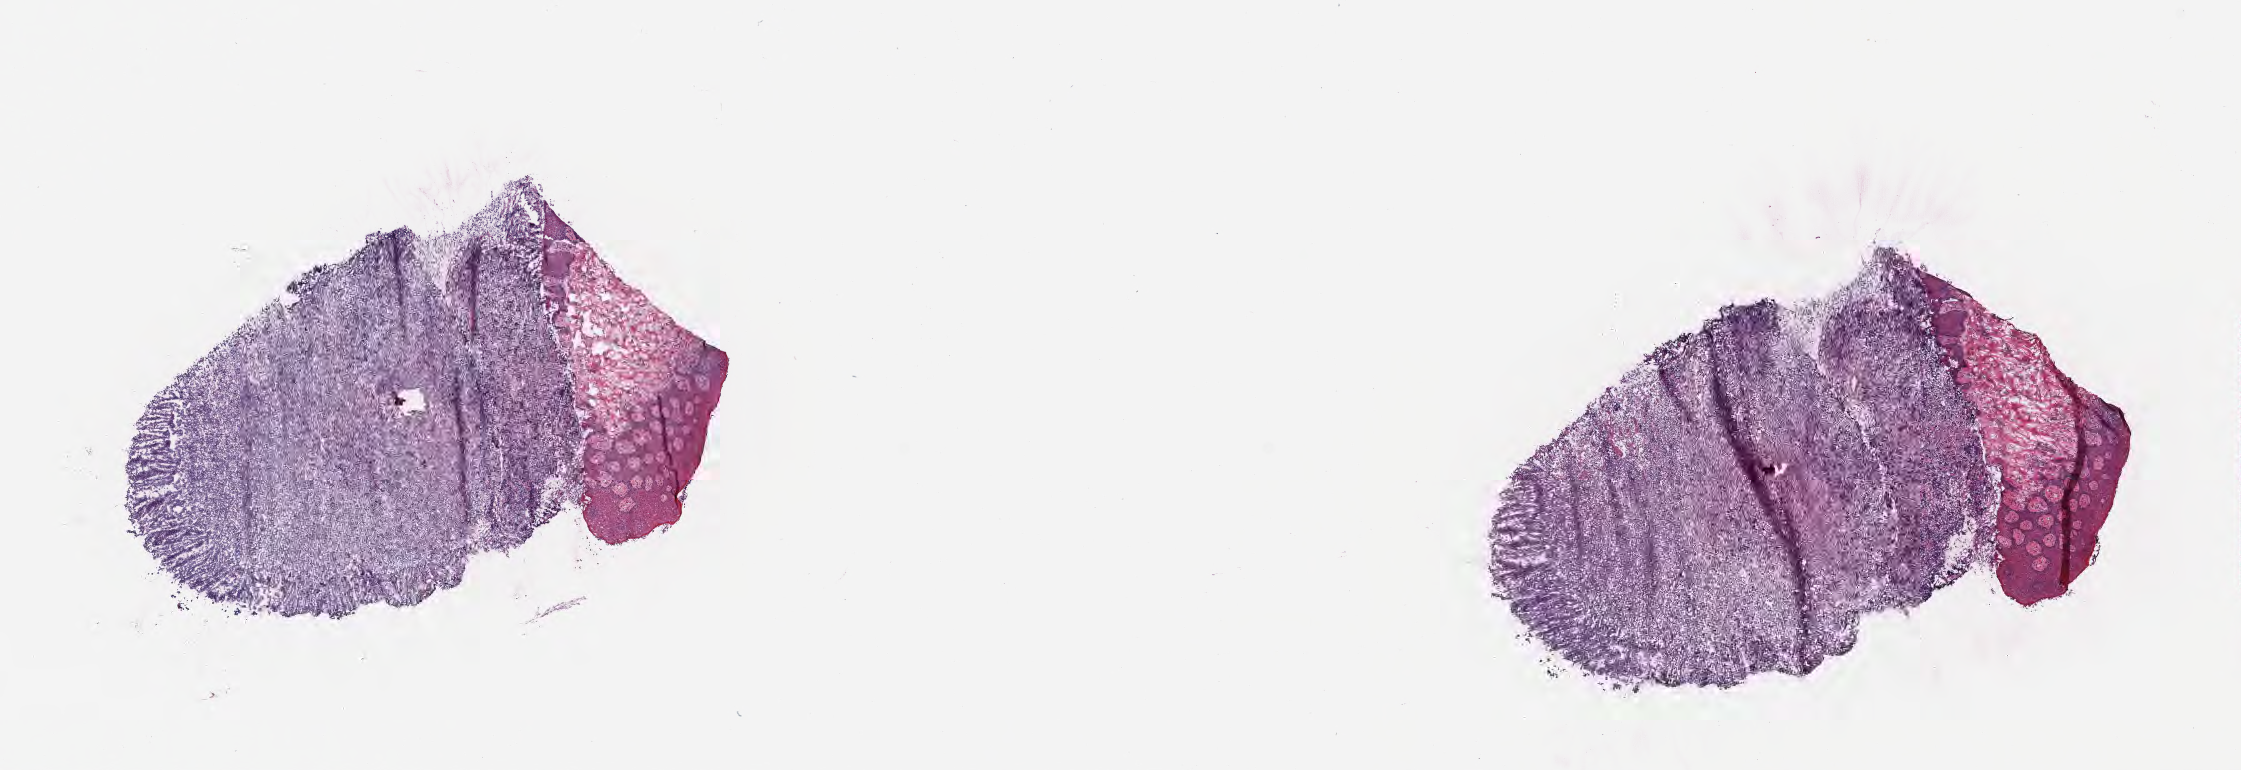
Haematoxylin and eosin whole-slide image, shown as a low-resolution overview of the whole scanned area (about 18.1 x 6.2 mm), frozen section (tissue freezing medium), specimen: primary tumor, site: gum of mandible. Male patient, aged 10. Slide review estimates, as recorded: tumor cells 70%, tumor nuclei 80%, stromal cells 10%, necrosis 10%, normal cells 10%. Infiltration values recorded for this section: lymphocyte infiltration 40%, monocyte infiltration 15%, neutrophil infiltration 5%.
• diagnosis: Burkitt lymphoma, NOS
• Ann Arbor stage (patient): Stage IV